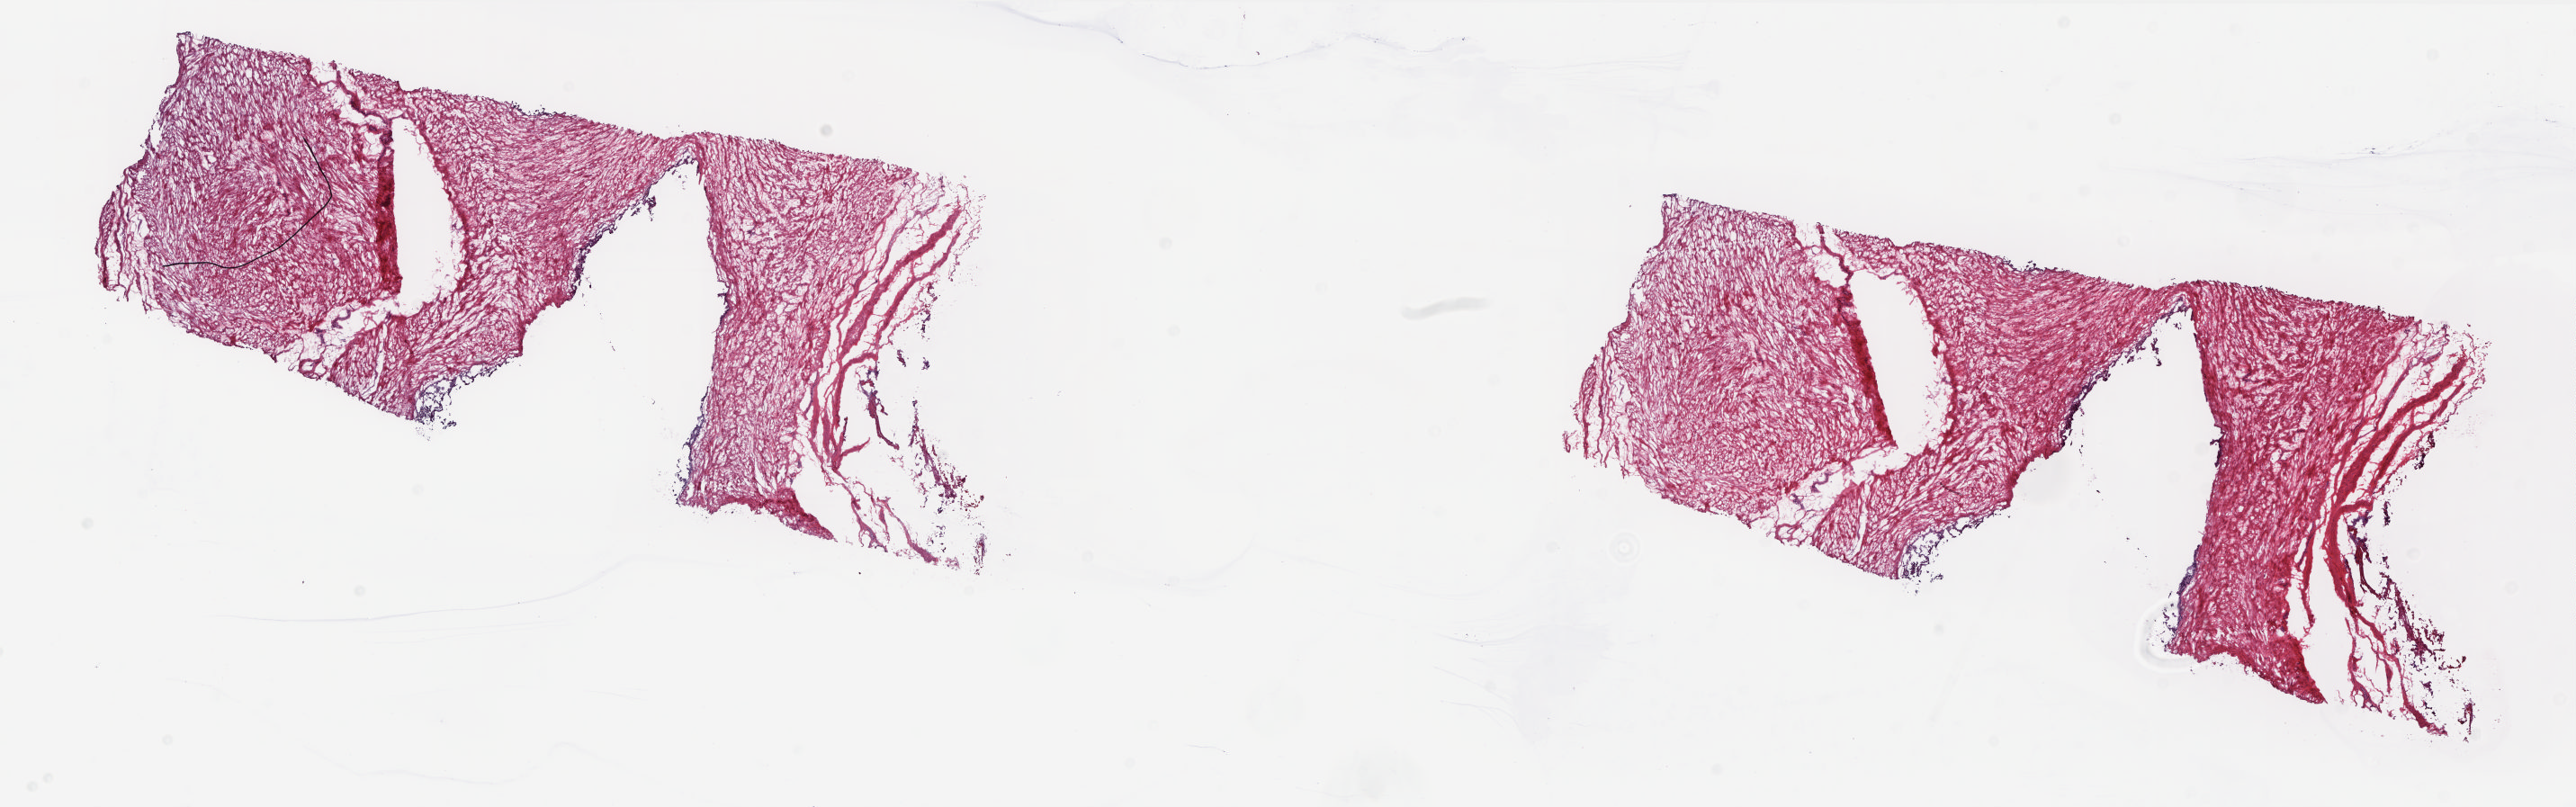
Digitized H&E tissue section (whole slide), whole scanned area (about 23.1 x 7.2 mm) shown as a low-resolution overview. Frozen section from the top of the tissue portion. Solid tissue normal (non-tumour tissue) sample from the prostate. Male patient; age at initial diagnosis 55 years. Pathologist review of this section (percent, as recorded): tumour cells 0%, tumour nuclei 0%, normal cells 10%, stromal cells 90%, necrosis 0%. Infiltration values recorded for this section: lymphocyte infiltration 0%, monocyte infiltration 0%, neutrophil infiltration 0%.
• this section: solid tissue normal sample (biorepository sample class)
• patient diagnosis: Adenocarcinoma, NOS